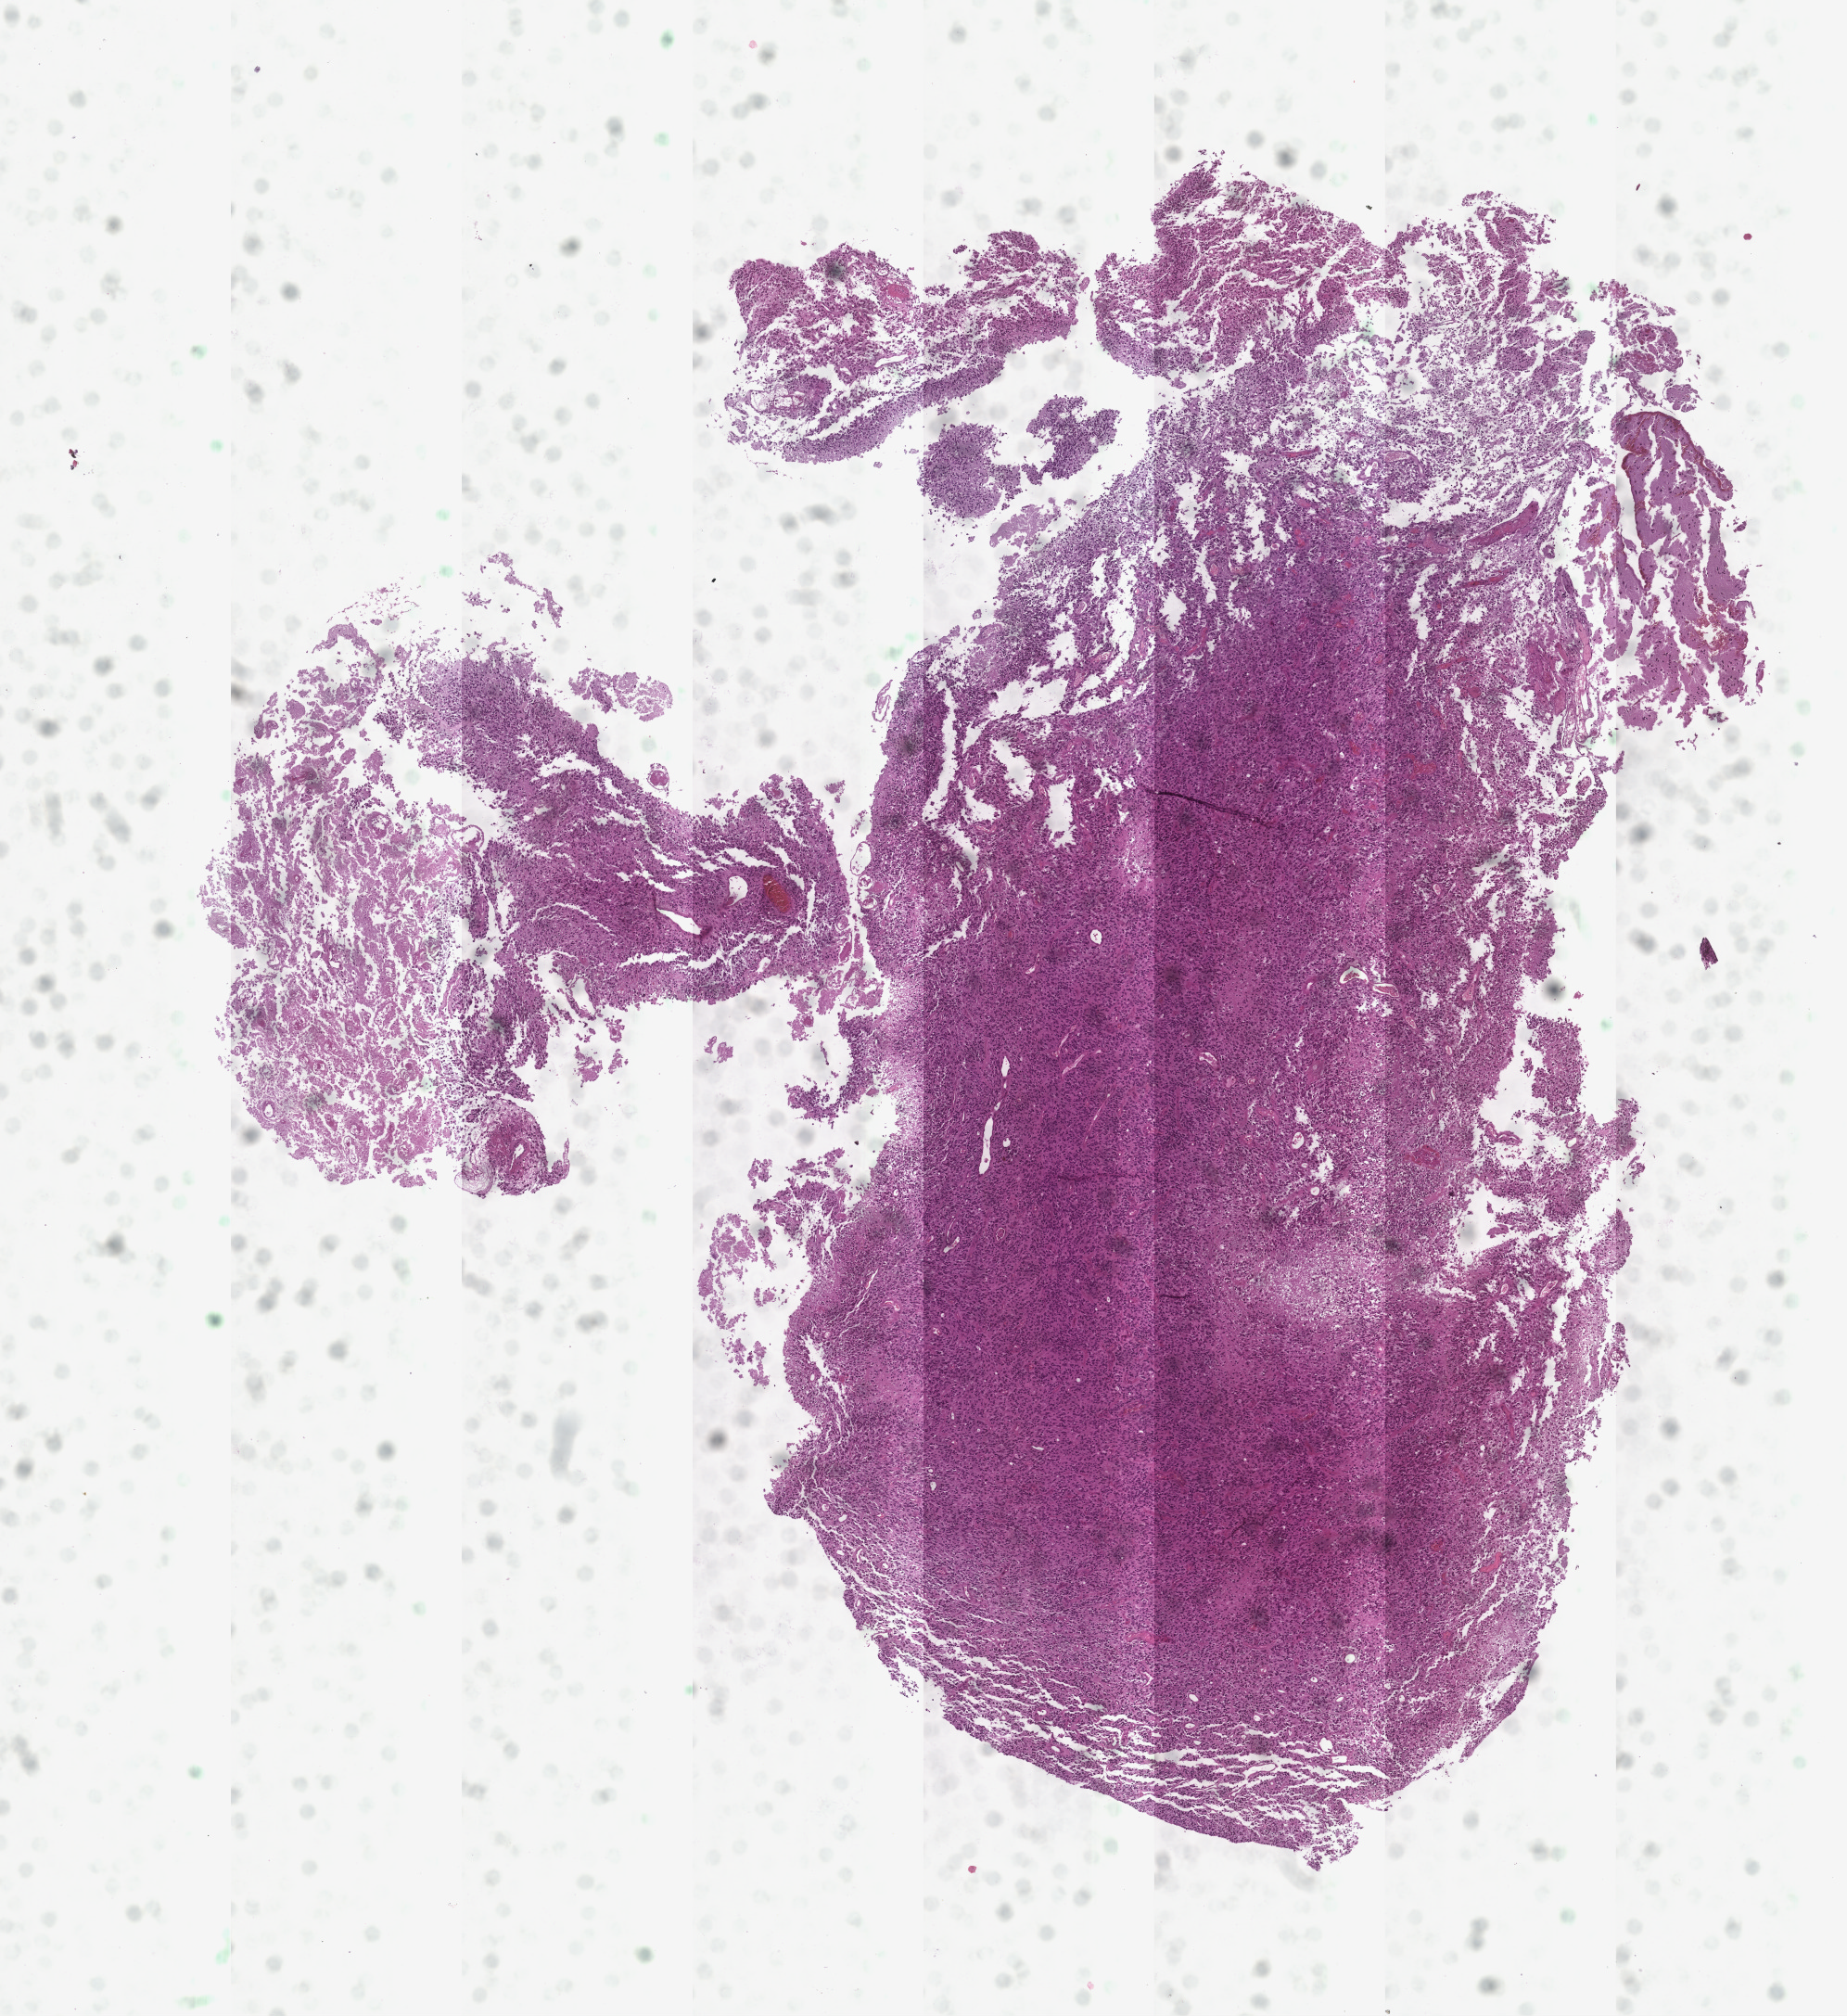
H&E whole-slide image, whole scanned area (about 8.0 x 8.8 mm) shown as a low-resolution overview; brain, tumour tissue. Female, 63 y/o.
• histologic diagnosis: Glioblastoma